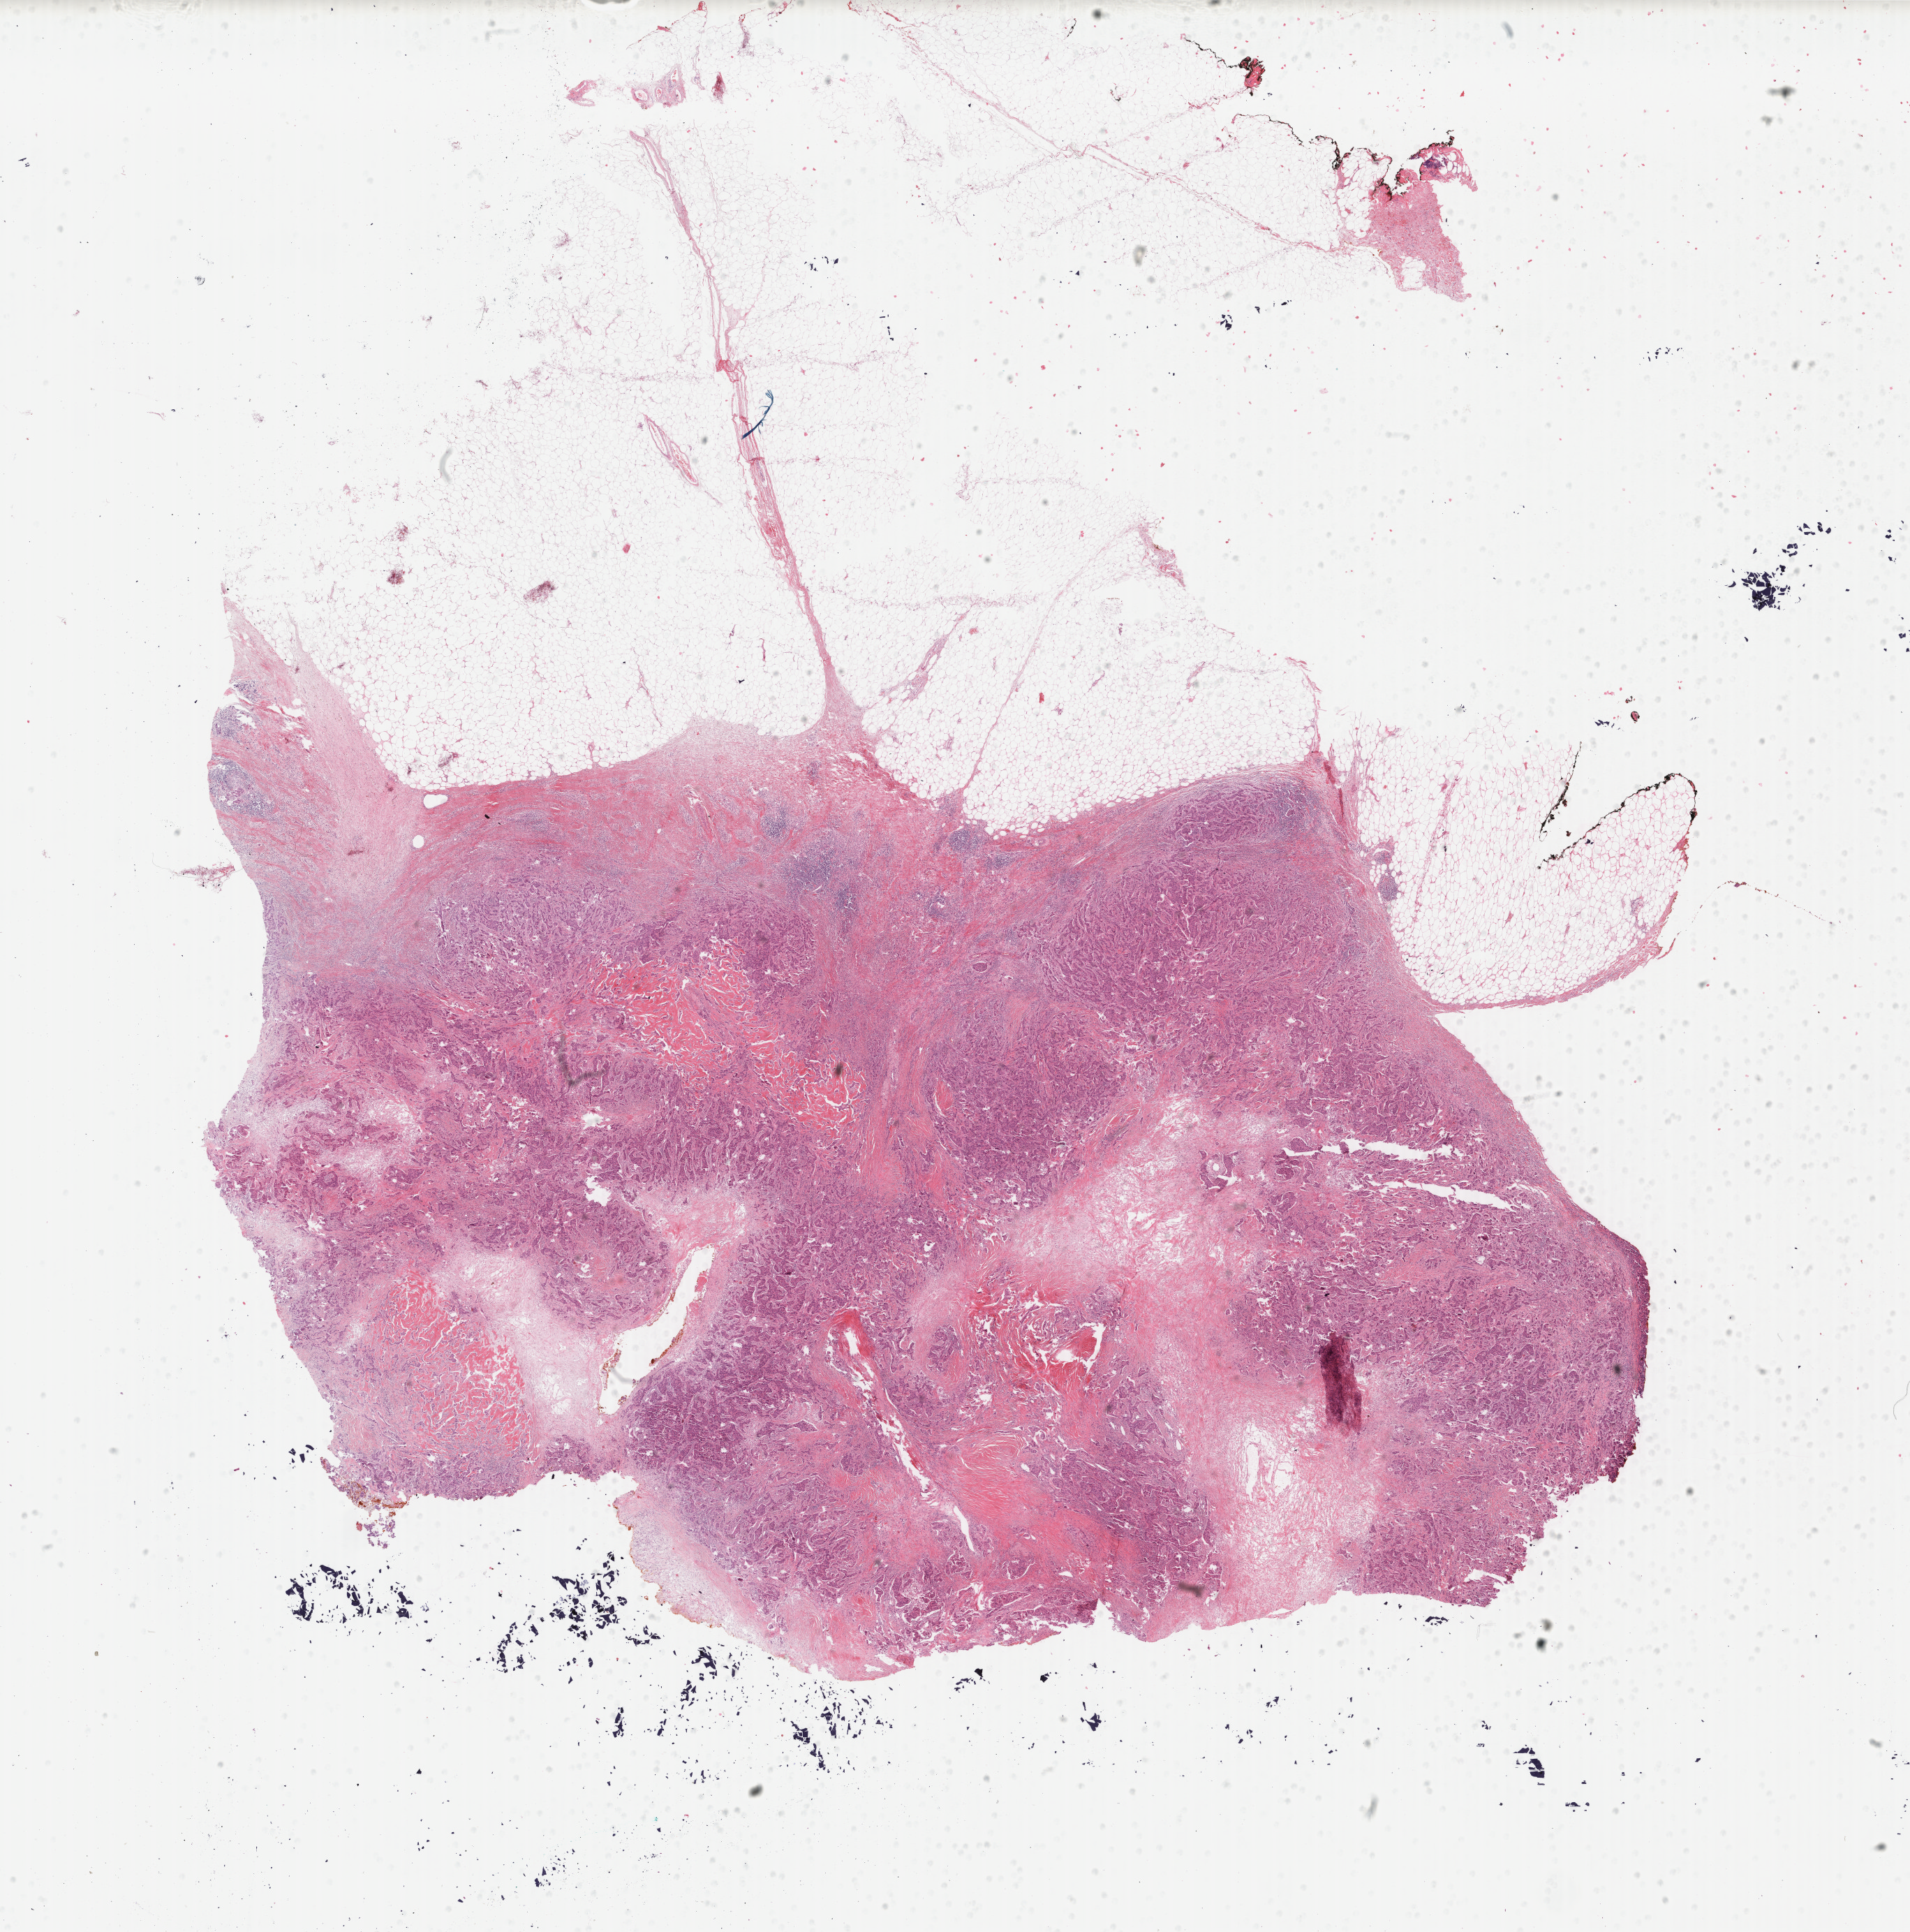
Digitized H&E-stained tissue section (whole slide) — whole scanned area (about 21.7 x 22.0 mm, slide scanned at 40x) shown as a low-resolution overview. Formalin-fixed paraffin-embedded (FFPE) diagnostic section. Sample: primary tumour, breast. Female, age 55 years at initial diagnosis.
AJCC pathologic stage: IIIC. TNM: T3 N3 M0. Pathologic diagnosis: Infiltrating duct carcinoma, NOS.